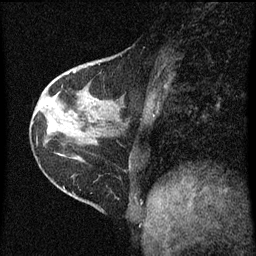
Breast MRI (dynamic contrast-enhanced), one sagittal slice; position 26 of 60 along the scan axis; dynamic contrast-enhanced series, image 2 of 3 at this slice position (ordered by acquisition); 1.5 T; TE 4.2 ms, TR 8 ms; 2 mm slice thickness; 256 × 256 image matrix. Patient: female, 38 years.
Outlined on this slice (semi-automatically segmented with operator editing):
- analysis volume of interest (the breast-tissue region the enhancement analysis was run in; not a lesion): bounding box [x1, y1, x2, y2] px = [67, 48, 130, 131]
- tumour enhancement mask (voxels above the 70 % enhancement threshold inside the analysis volume of interest): [74, 70, 76, 73]